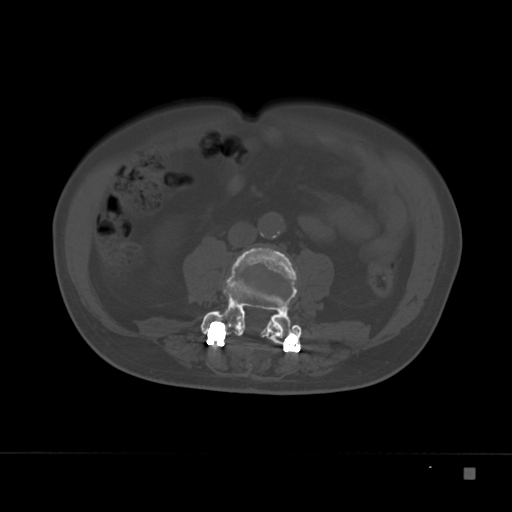
CT including the spine, one axial slice. Reconstruction kernel Br40s. Bone window (W 1800 / L 400 HU). 1.5 mm slice thickness. 512 × 512 image matrix, field of view 389 × 389 mm. Male patient, age 72 years. Case-level facts recorded for this patient, not image findings: primary cancer: skeletal.
Outlined on this slice (semi-automatic segmentation, software-assisted and operator-edited):
- L3 vertebra: bounding box <232,246,298,329> (left, top, right, bottom; pixels)
- L4 vertebra: <201,266,302,345>